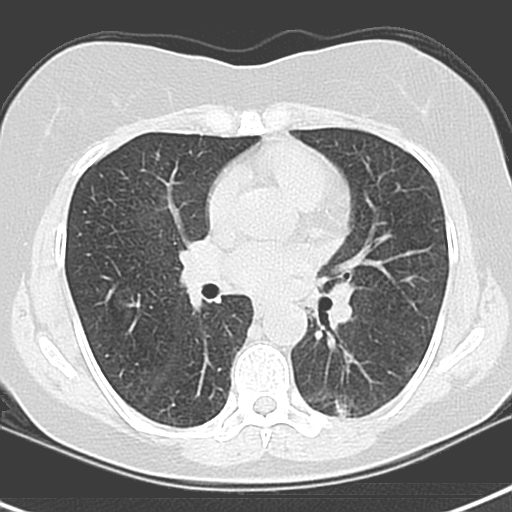
Chest CT (low-dose screening protocol), one axial image, first (baseline) screen, lung window (W 1500 / L -600 HU), 3.2 mm slice thickness. Female, age 55 years at enrolment. Current smoker at enrolment.
Lesion marked by an expert reader, bounding box [x1, y1, x2, y2] px = [307, 374, 384, 424]. The screening reader recorded 3 non-calcified nodules or masses ≥4 mm on this exam (left upper lobe, left lower lobe, left lower lobe); which of them this box marks is not recorded. Official screen result: positive, change unspecified: nodule(s) >= 4 mm or enlarging nodule(s), mass(es), or other non-specific abnormalities suspicious for lung cancer. Later outcome: lung cancer diagnosed 1063 days after this screen — adenocarcinoma with mixed subtypes, left lower lobe, poorly differentiated (G3), stage IA (AJCC 6th edition), 21 mm at pathology.